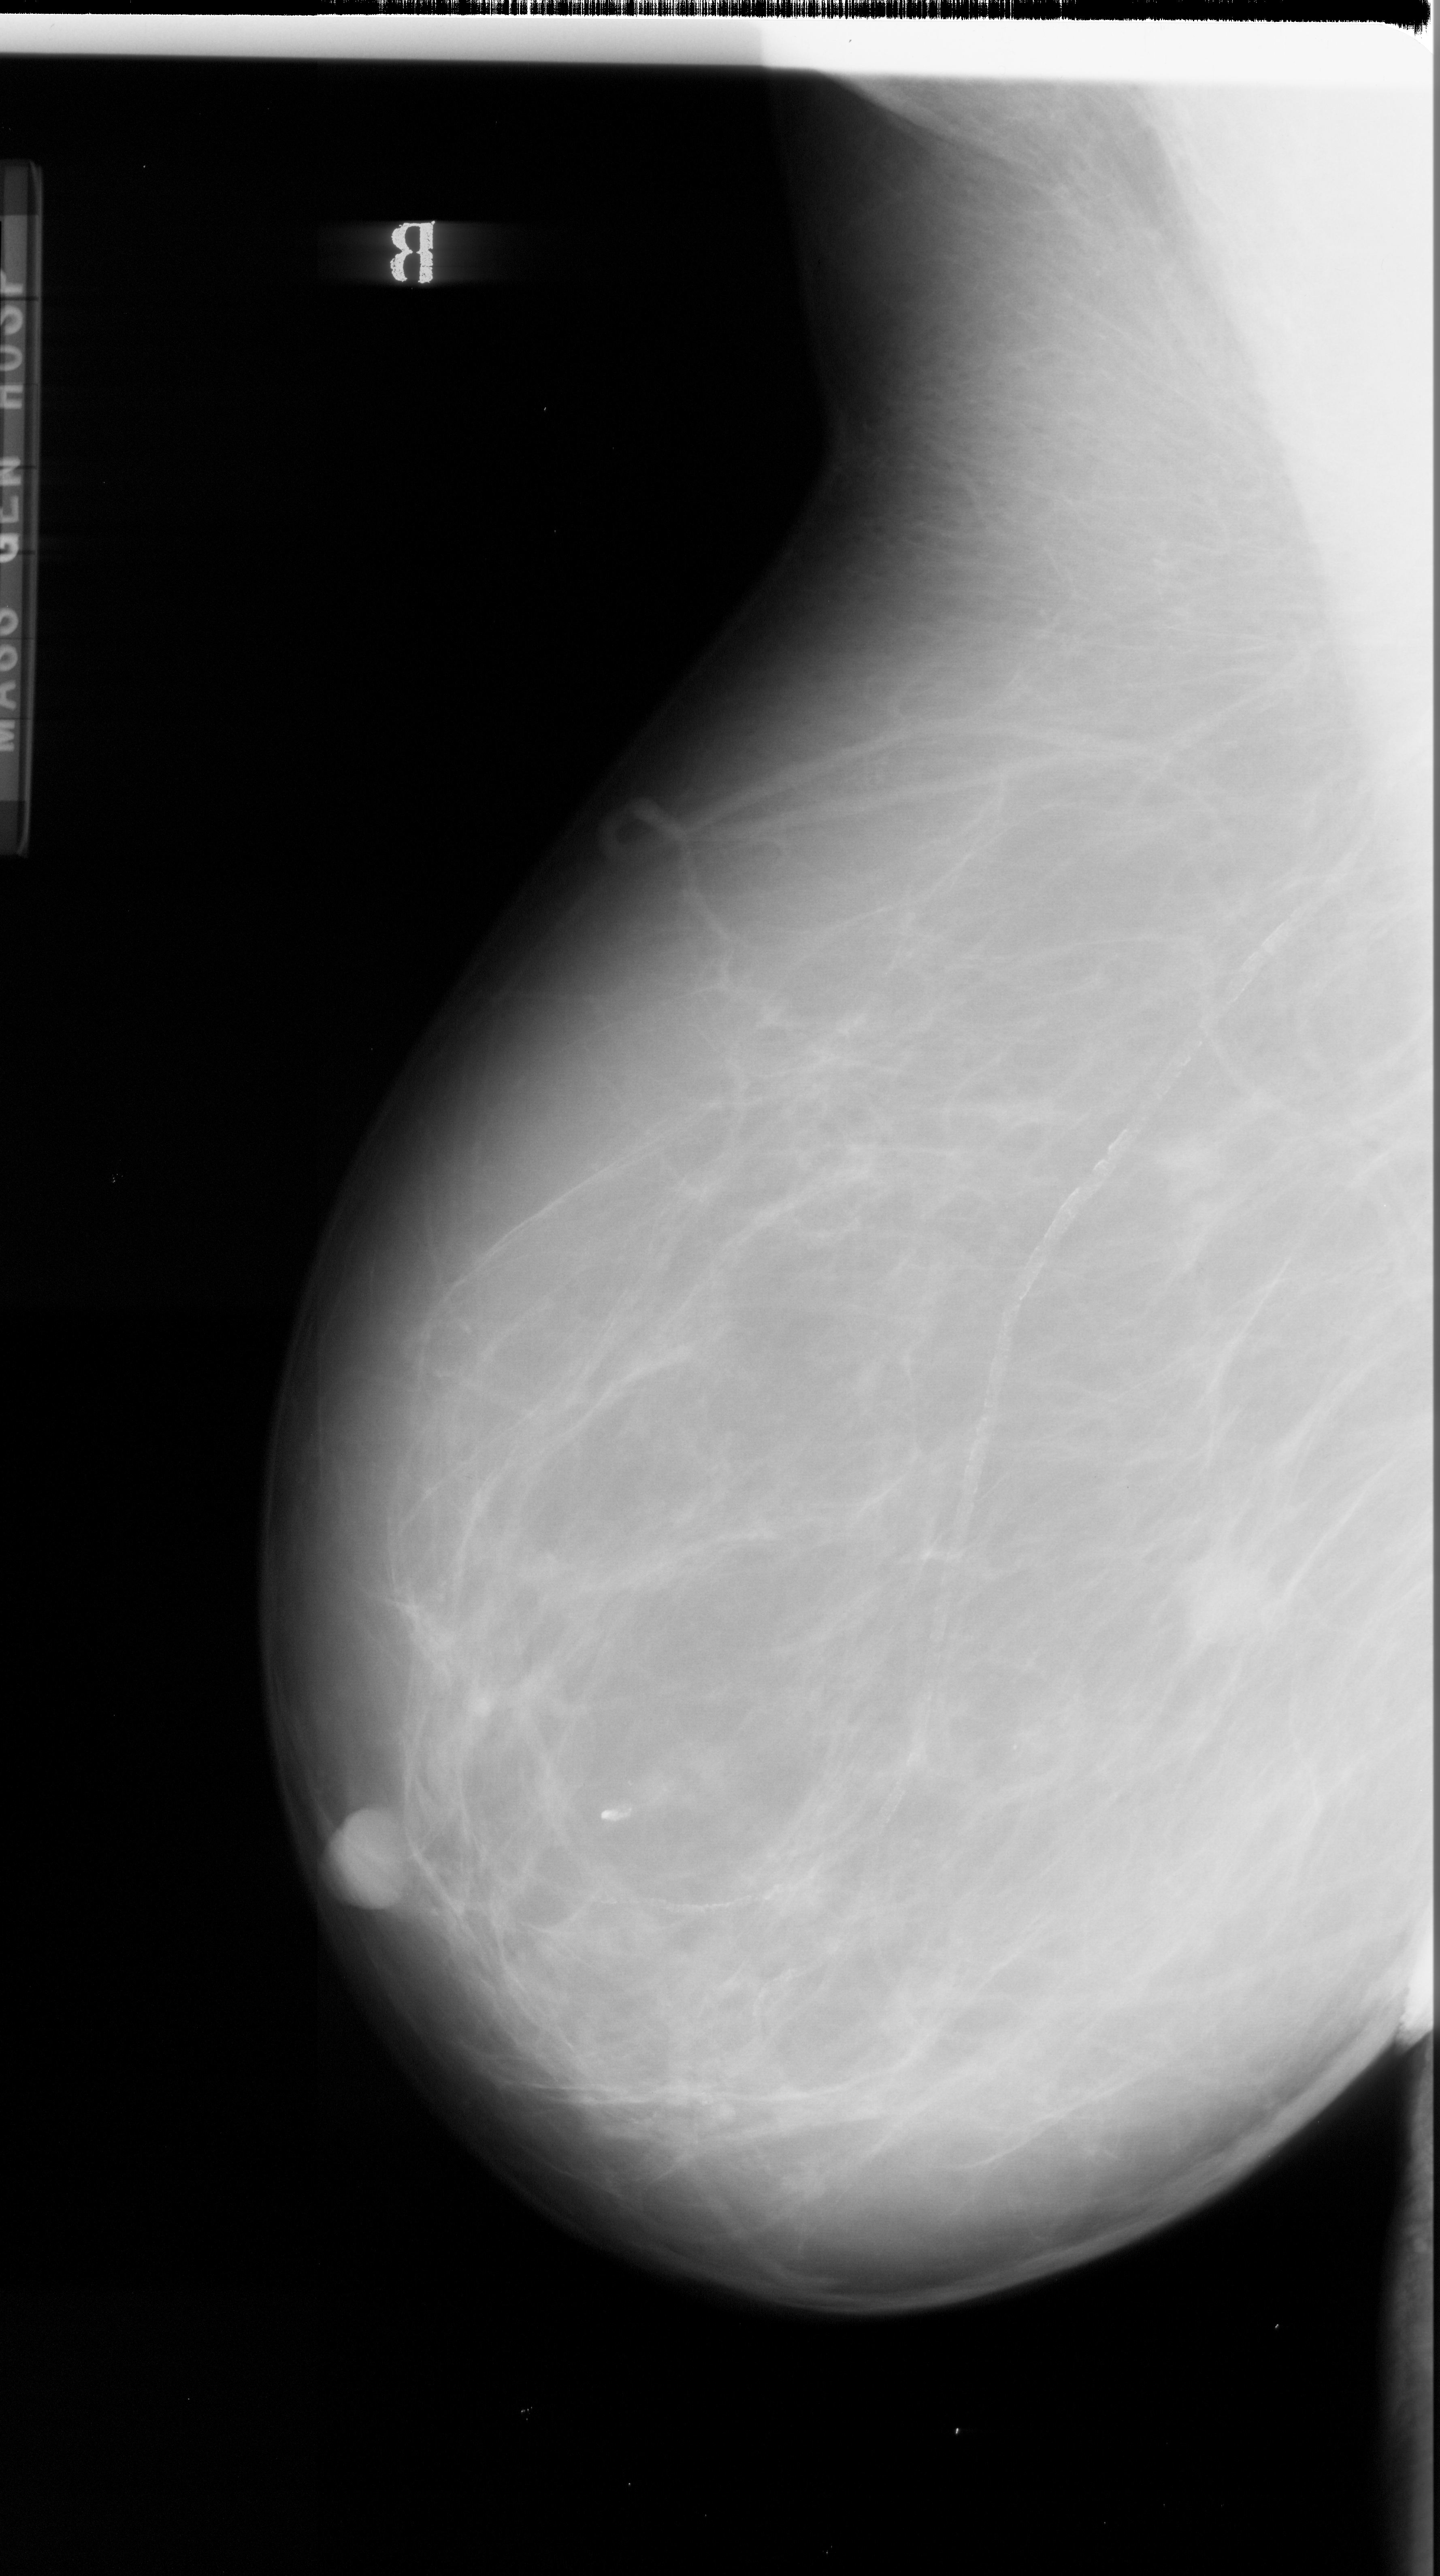
Digitized screen-film mammogram; left breast; mediolateral oblique (MLO) view; breast composition: almost entirely fatty (BI-RADS density category 1 of 4); 1440 × 2576 image matrix.
Marked abnormalities (boxes around the expert regions of interest):
- mass, shape irregular, margins spiculated; BI-RADS assessment category 5; subtlety rating 4 on a 1 (subtle) to 5 (obvious) scale; pathology (as recorded): malignant: bounding box <1169,1544,1265,1656> (left, top, right, bottom; pixels)